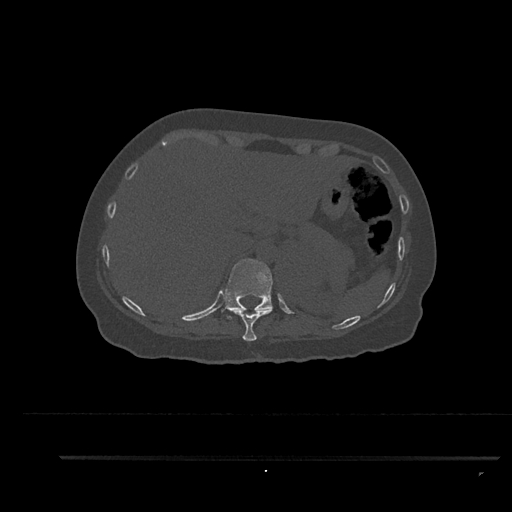
CT including the spine, one axial slice; reconstruction kernel Br40s/3; 120 kVp; bone window (W 1800 / L 400 HU); 0.5 mm slice thickness; 512 × 512 image matrix, field of view 408 × 408 mm. Female patient, age 44 years. From the clinical record (not read from this slice): primary cancer: renal.
Annotated regions visible in this slice (semi-automatically segmented with operator editing):
- T10 vertebra: bounding box (x1, y1, x2, y2) in pixels: (227, 308, 273, 341)
- T11 vertebra: (222, 259, 273, 319)